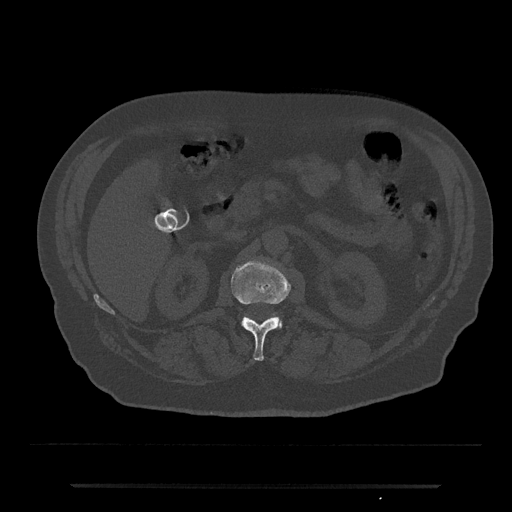
CT including the spine, one axial slice; position 521 of 797 along the scan axis; reconstruction kernel Br40s/3; bone window (W 1800 / L 400 HU); 0.5 mm slice thickness; 512 × 512 image matrix. Patient: male, 80 years. From the clinical record (not read from this slice): primary cancer: prostate; vertebrae with lytic lesions (as recorded): L1, T11.
Structures marked on this image (semi-automatic segmentation, software-assisted and operator-edited):
- L1 vertebra: bounding box <231,260,290,361> (left, top, right, bottom; pixels)
- L2 vertebra: <274,315,283,328>